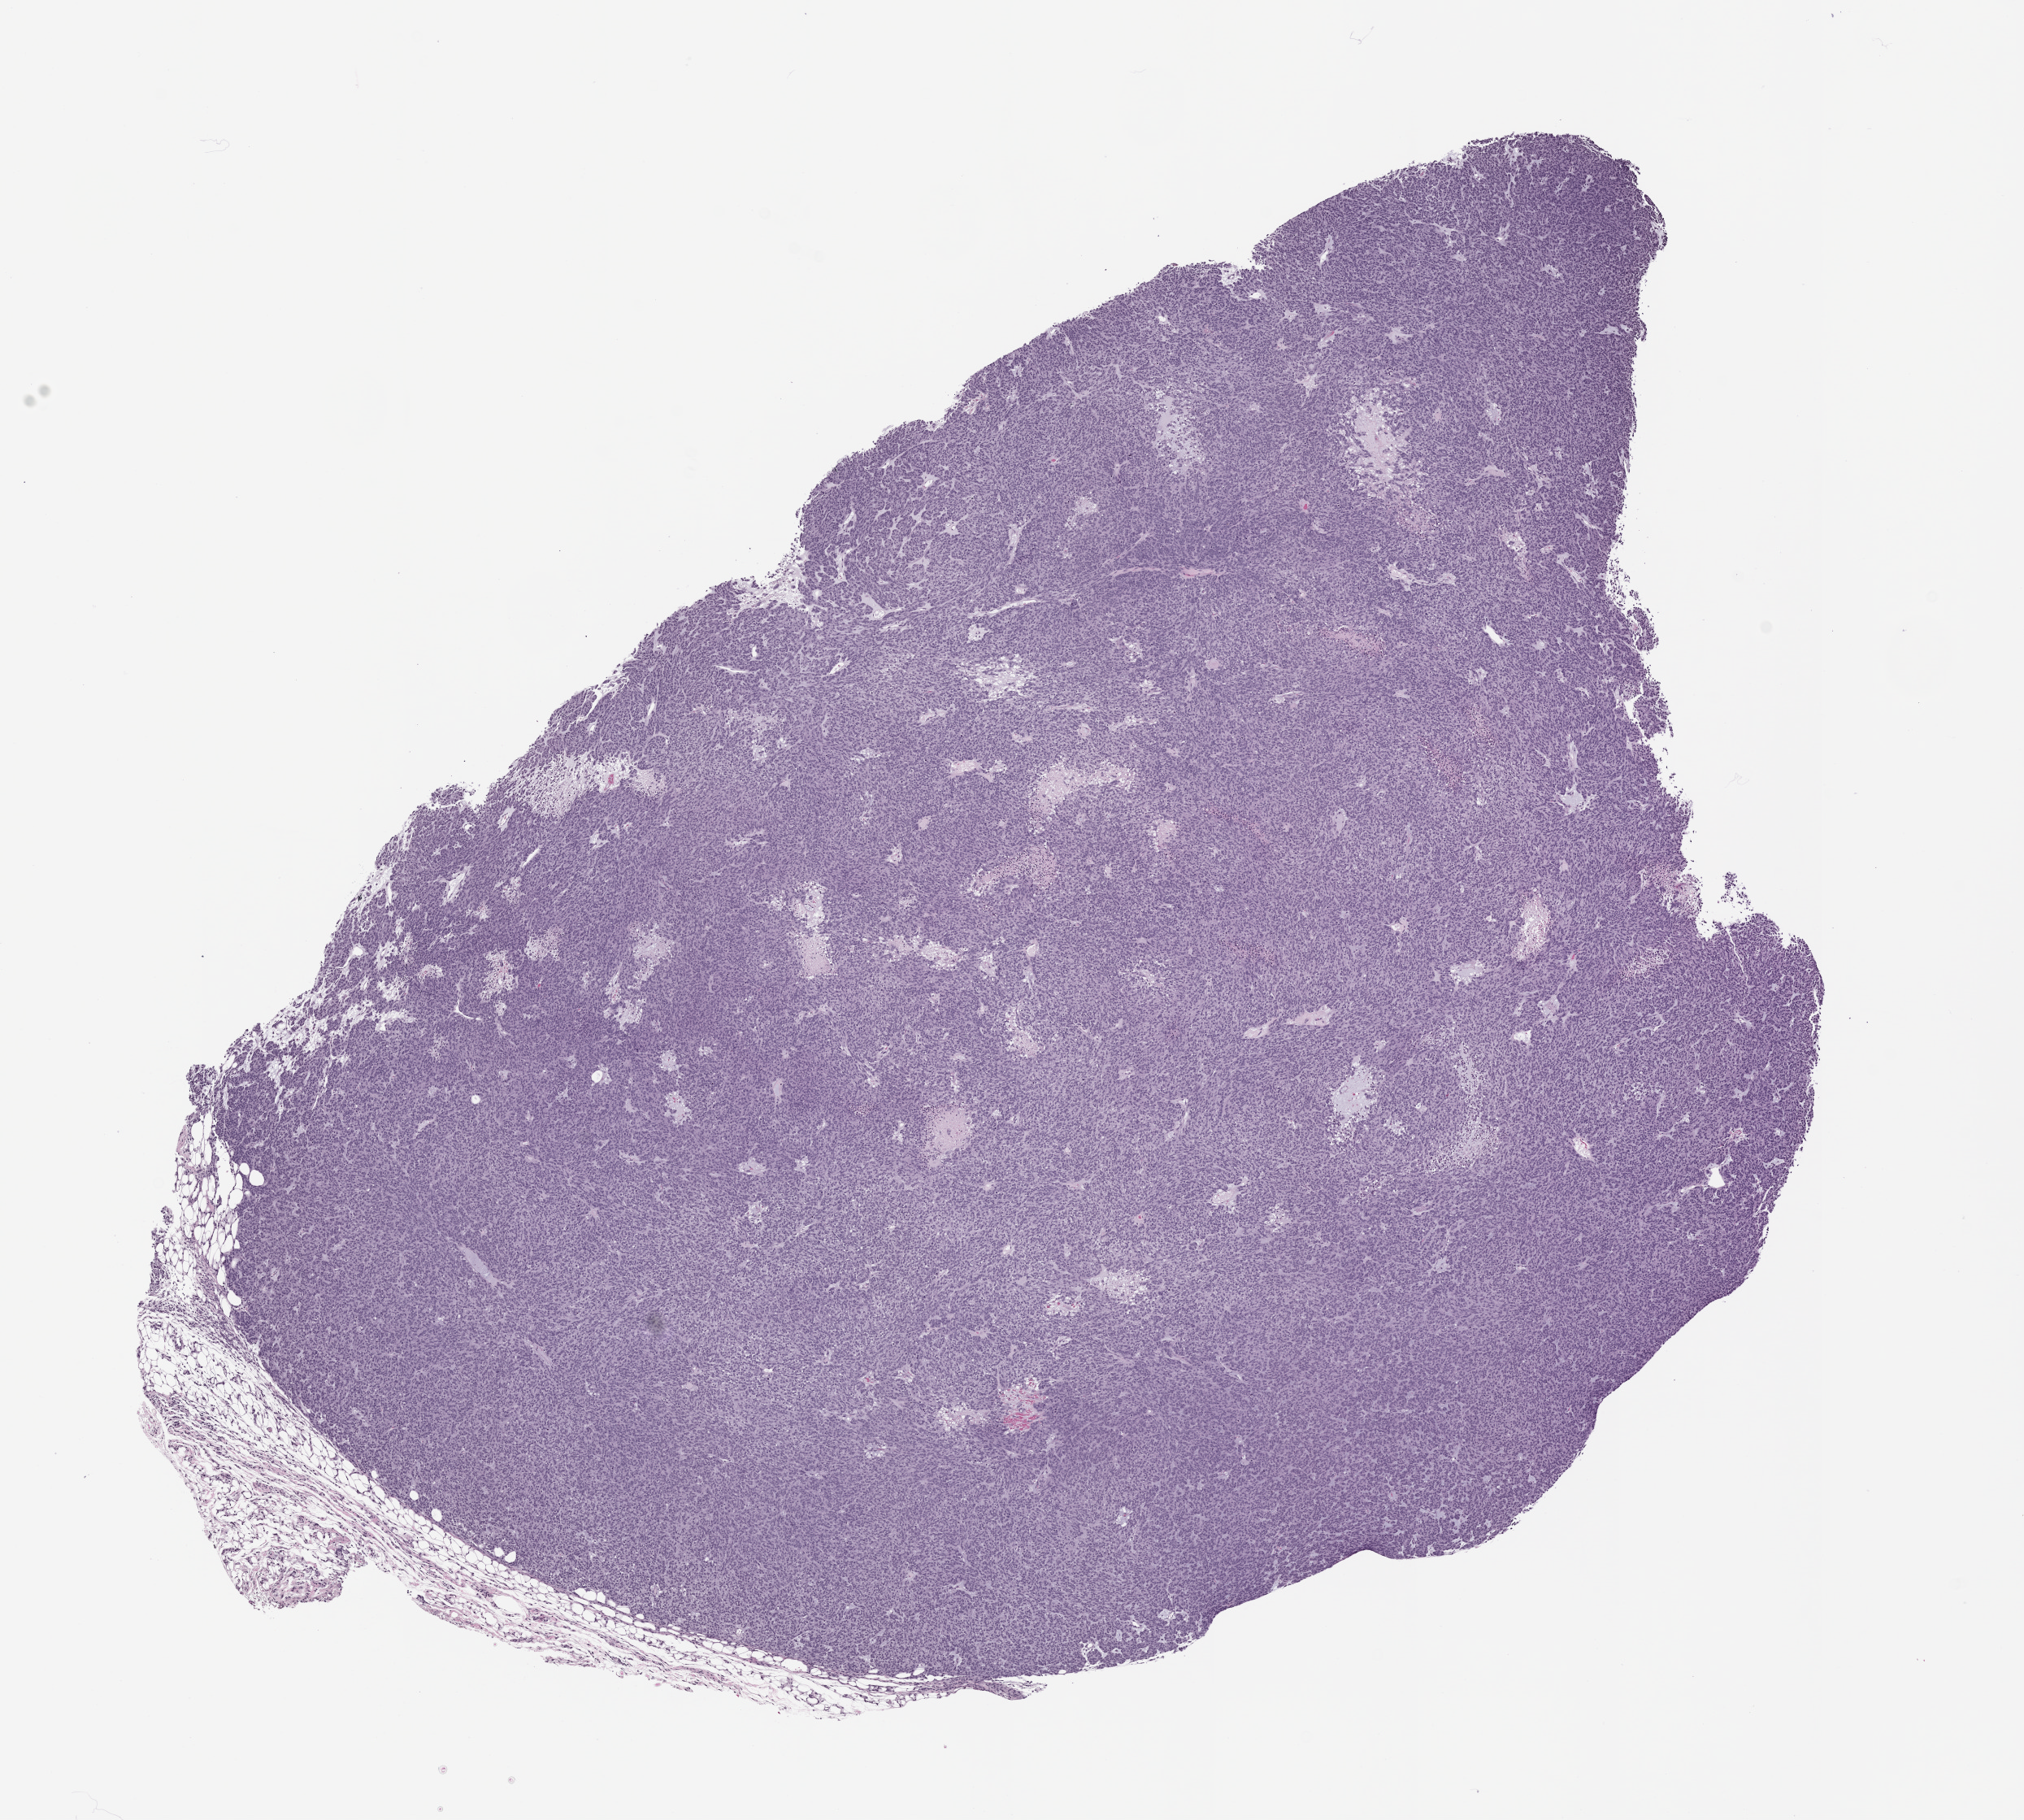
H&E whole-slide image of a patient-derived xenograft (PDX) tumor grown in a mouse, passage 0 — whole scanned area (about 10.0 x 9.0 mm) shown as a low-resolution overview, FFPE section, tumor site category: gastrointestinal tract.
Originating patient diagnosis: Gastrointestinal Stromal Tumor.